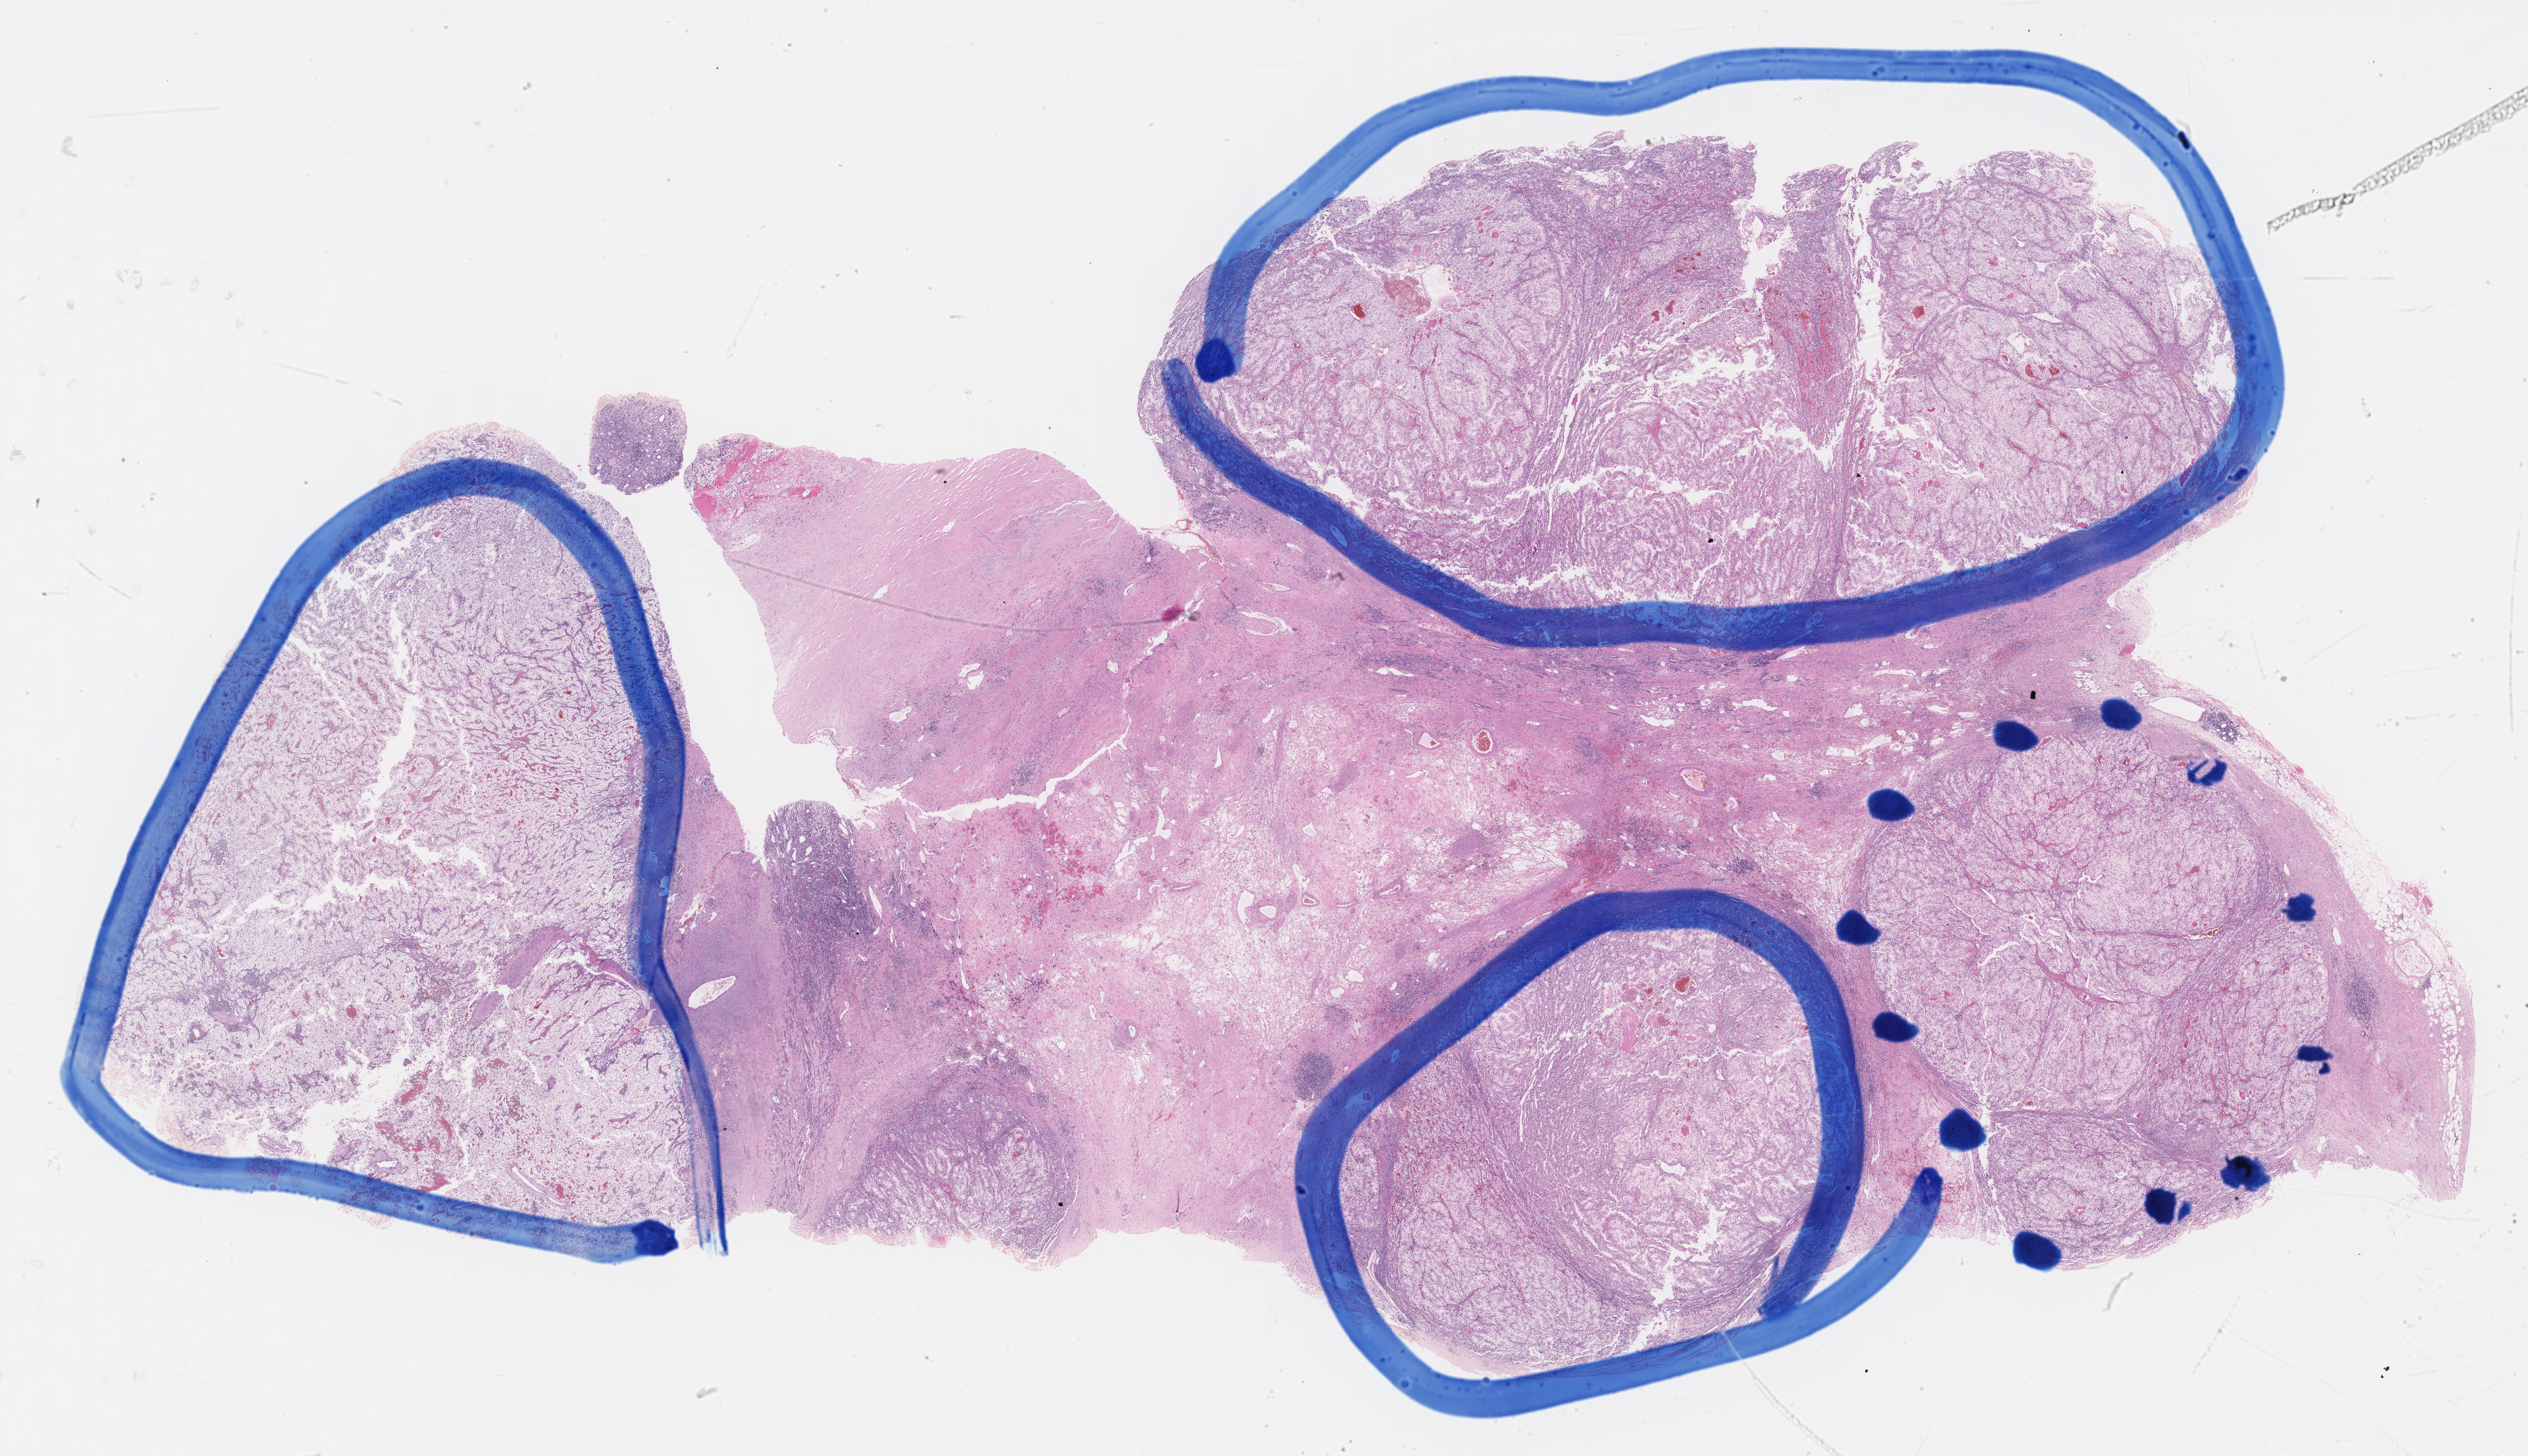
H&E-stained whole-slide image — low-resolution overview of the scanned area, about 30.2 x 17.4 mm, formalin-fixed paraffin-embedded (FFPE) diagnostic section, primary tumour sample from the kidney. Patient: male, age at initial diagnosis 47 years. Histologic grade: G3 (poorly differentiated).
Laterality: right. Histologic diagnosis: Clear cell adenocarcinoma, NOS. AJCC pathologic stage: III.